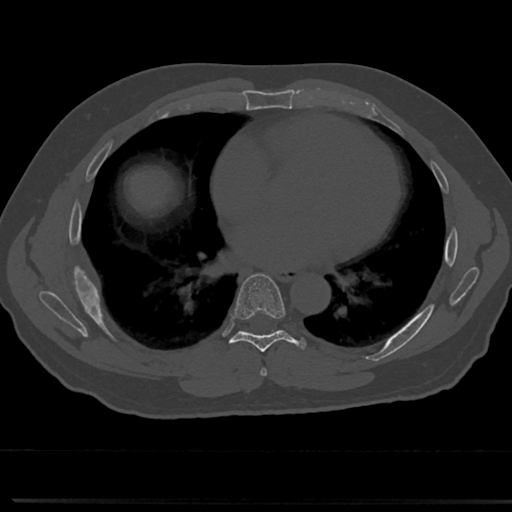
CT including the spine, one axial slice; position 402 of 817 along the scan axis; bone window (W 1800 / L 400 HU); 0.5 mm slice thickness; 512 × 512 image matrix. Male patient, age 61 years. Case-level facts recorded for this patient, not image findings: primary cancer: prostate.
Structures marked on this image (semi-automatic segmentation, software-assisted and operator-edited):
- T6 vertebra: bounding box [x1, y1, x2, y2] px = [260, 340, 319, 375]
- T7 vertebra: [214, 275, 309, 358]